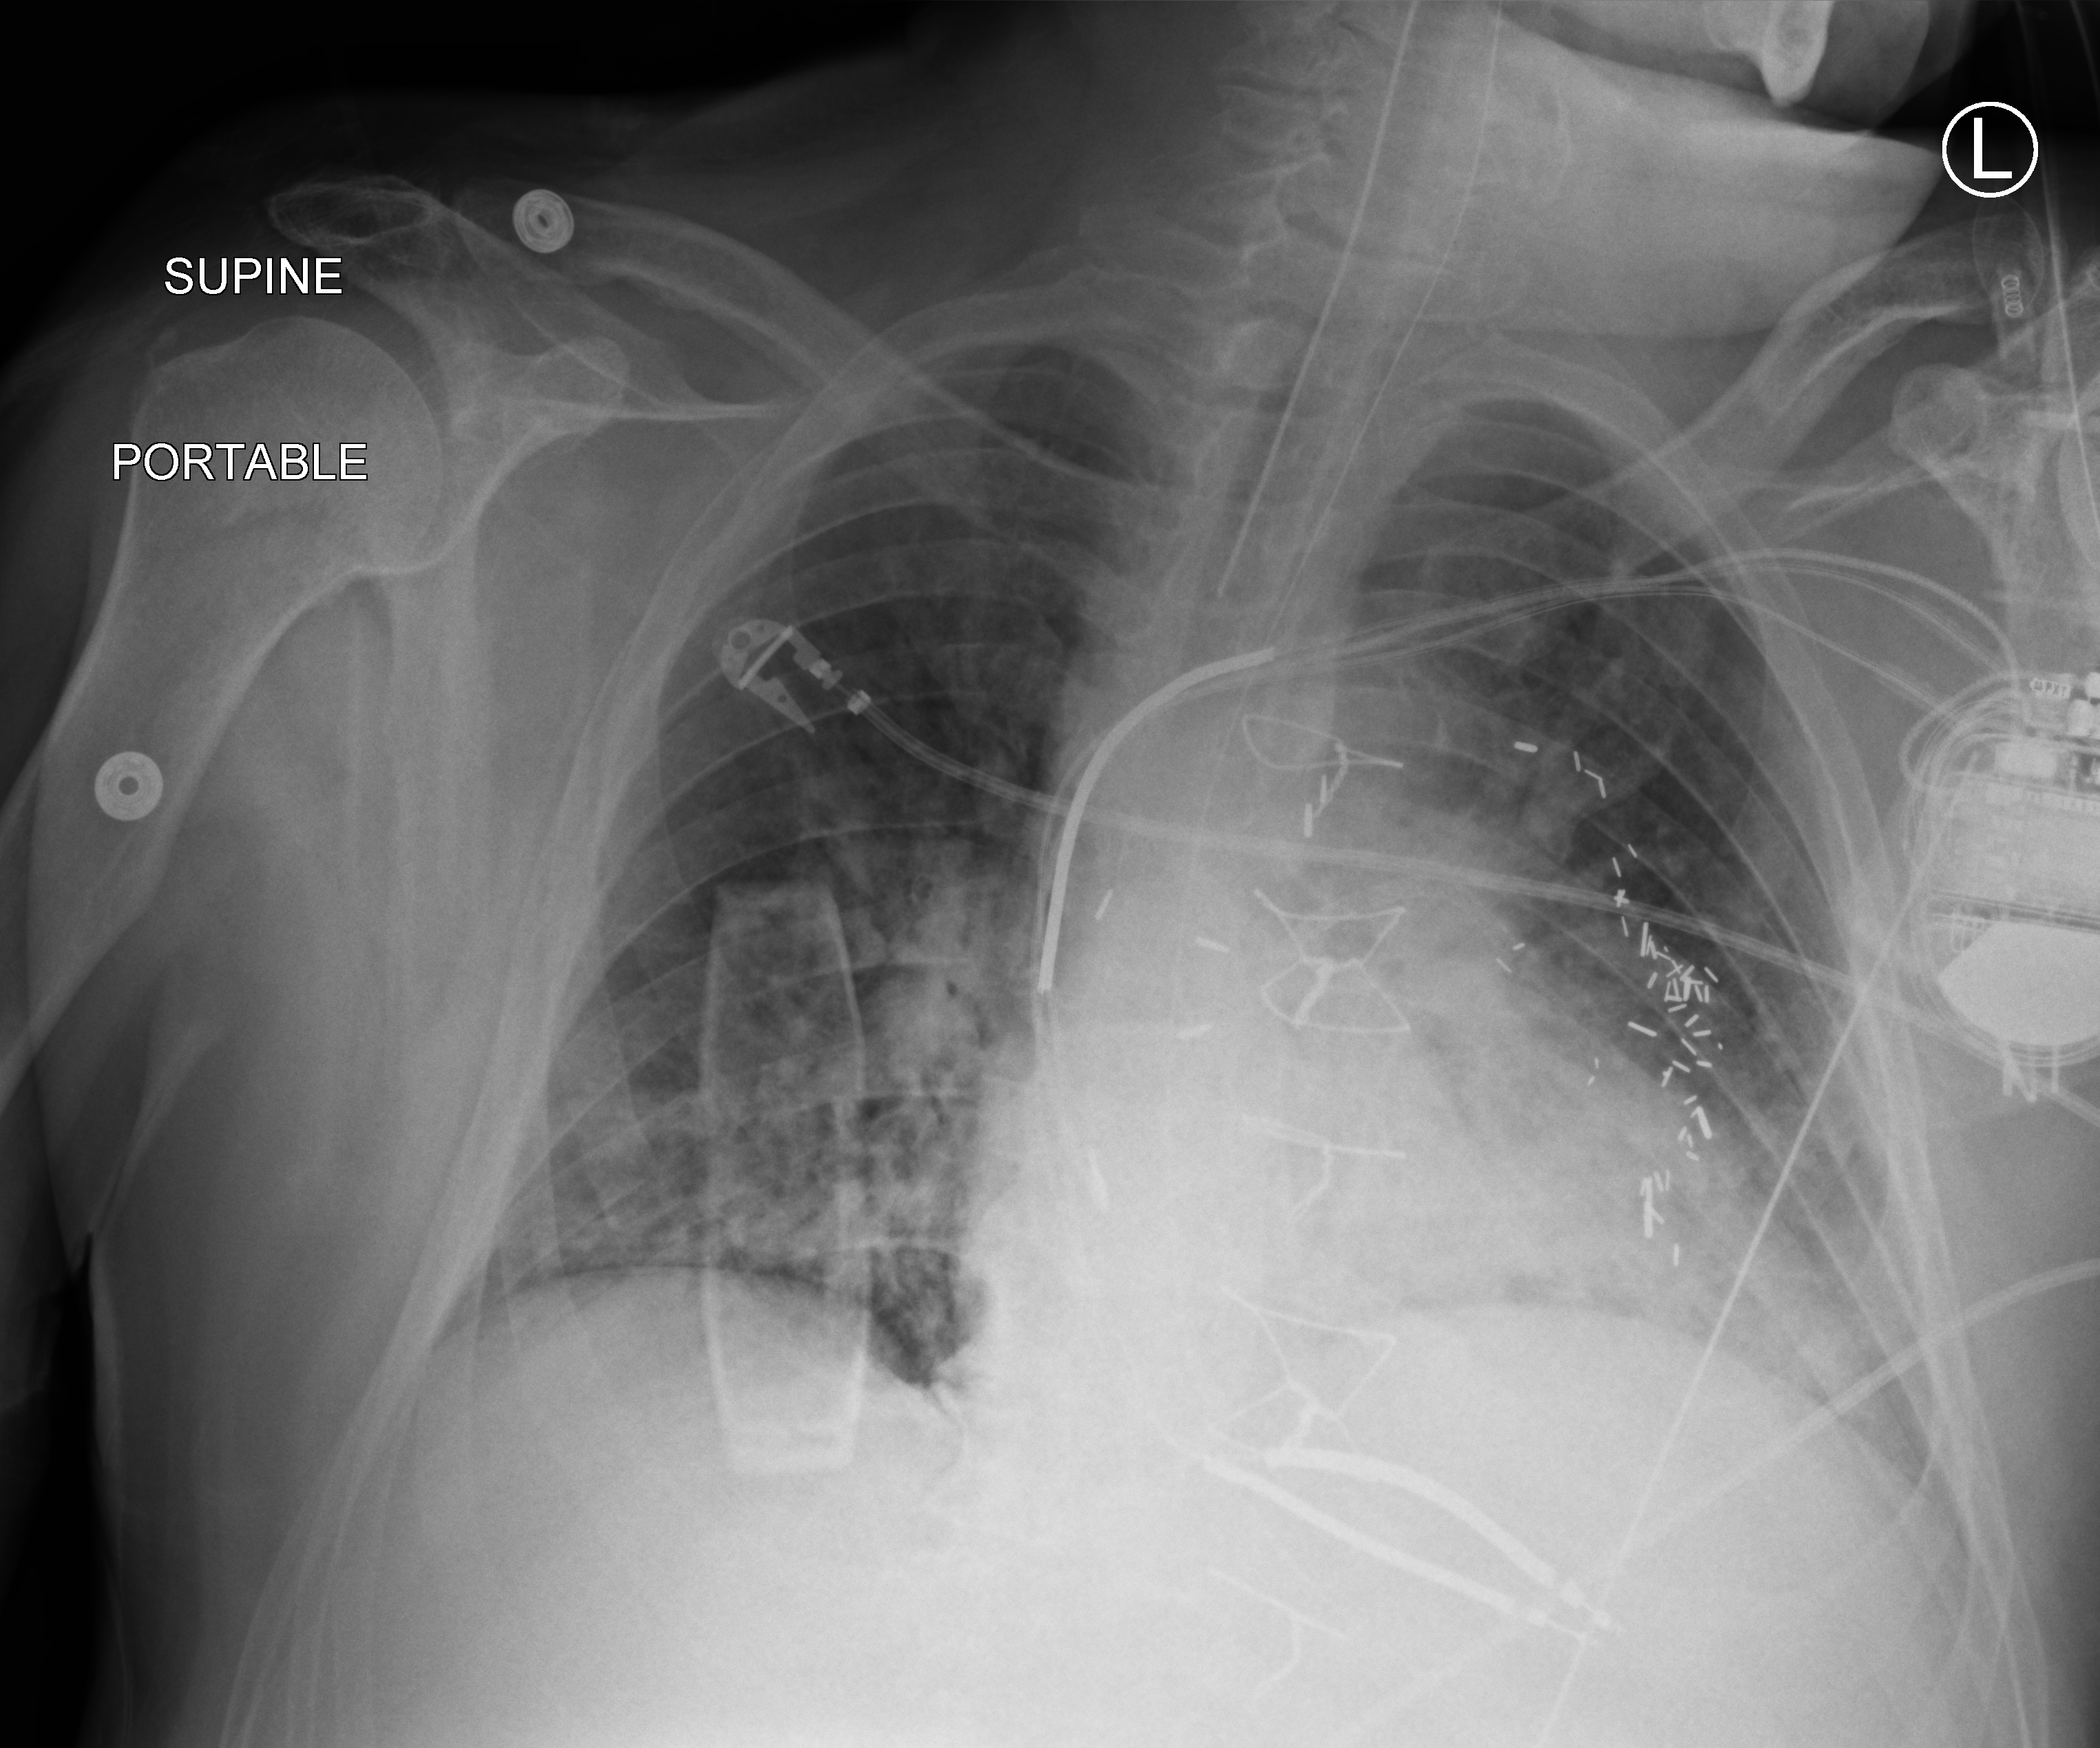
Bedside chest radiograph (computed radiography), anteroposterior (AP) projection. Male patient hospitalised with COVID-19, age 60–74 years.
Hospital-stay facts (about this admission, not read from this image; timing relative to this image not recorded): mechanically ventilated during this hospital stay: yes; length of hospital stay: 55 days.